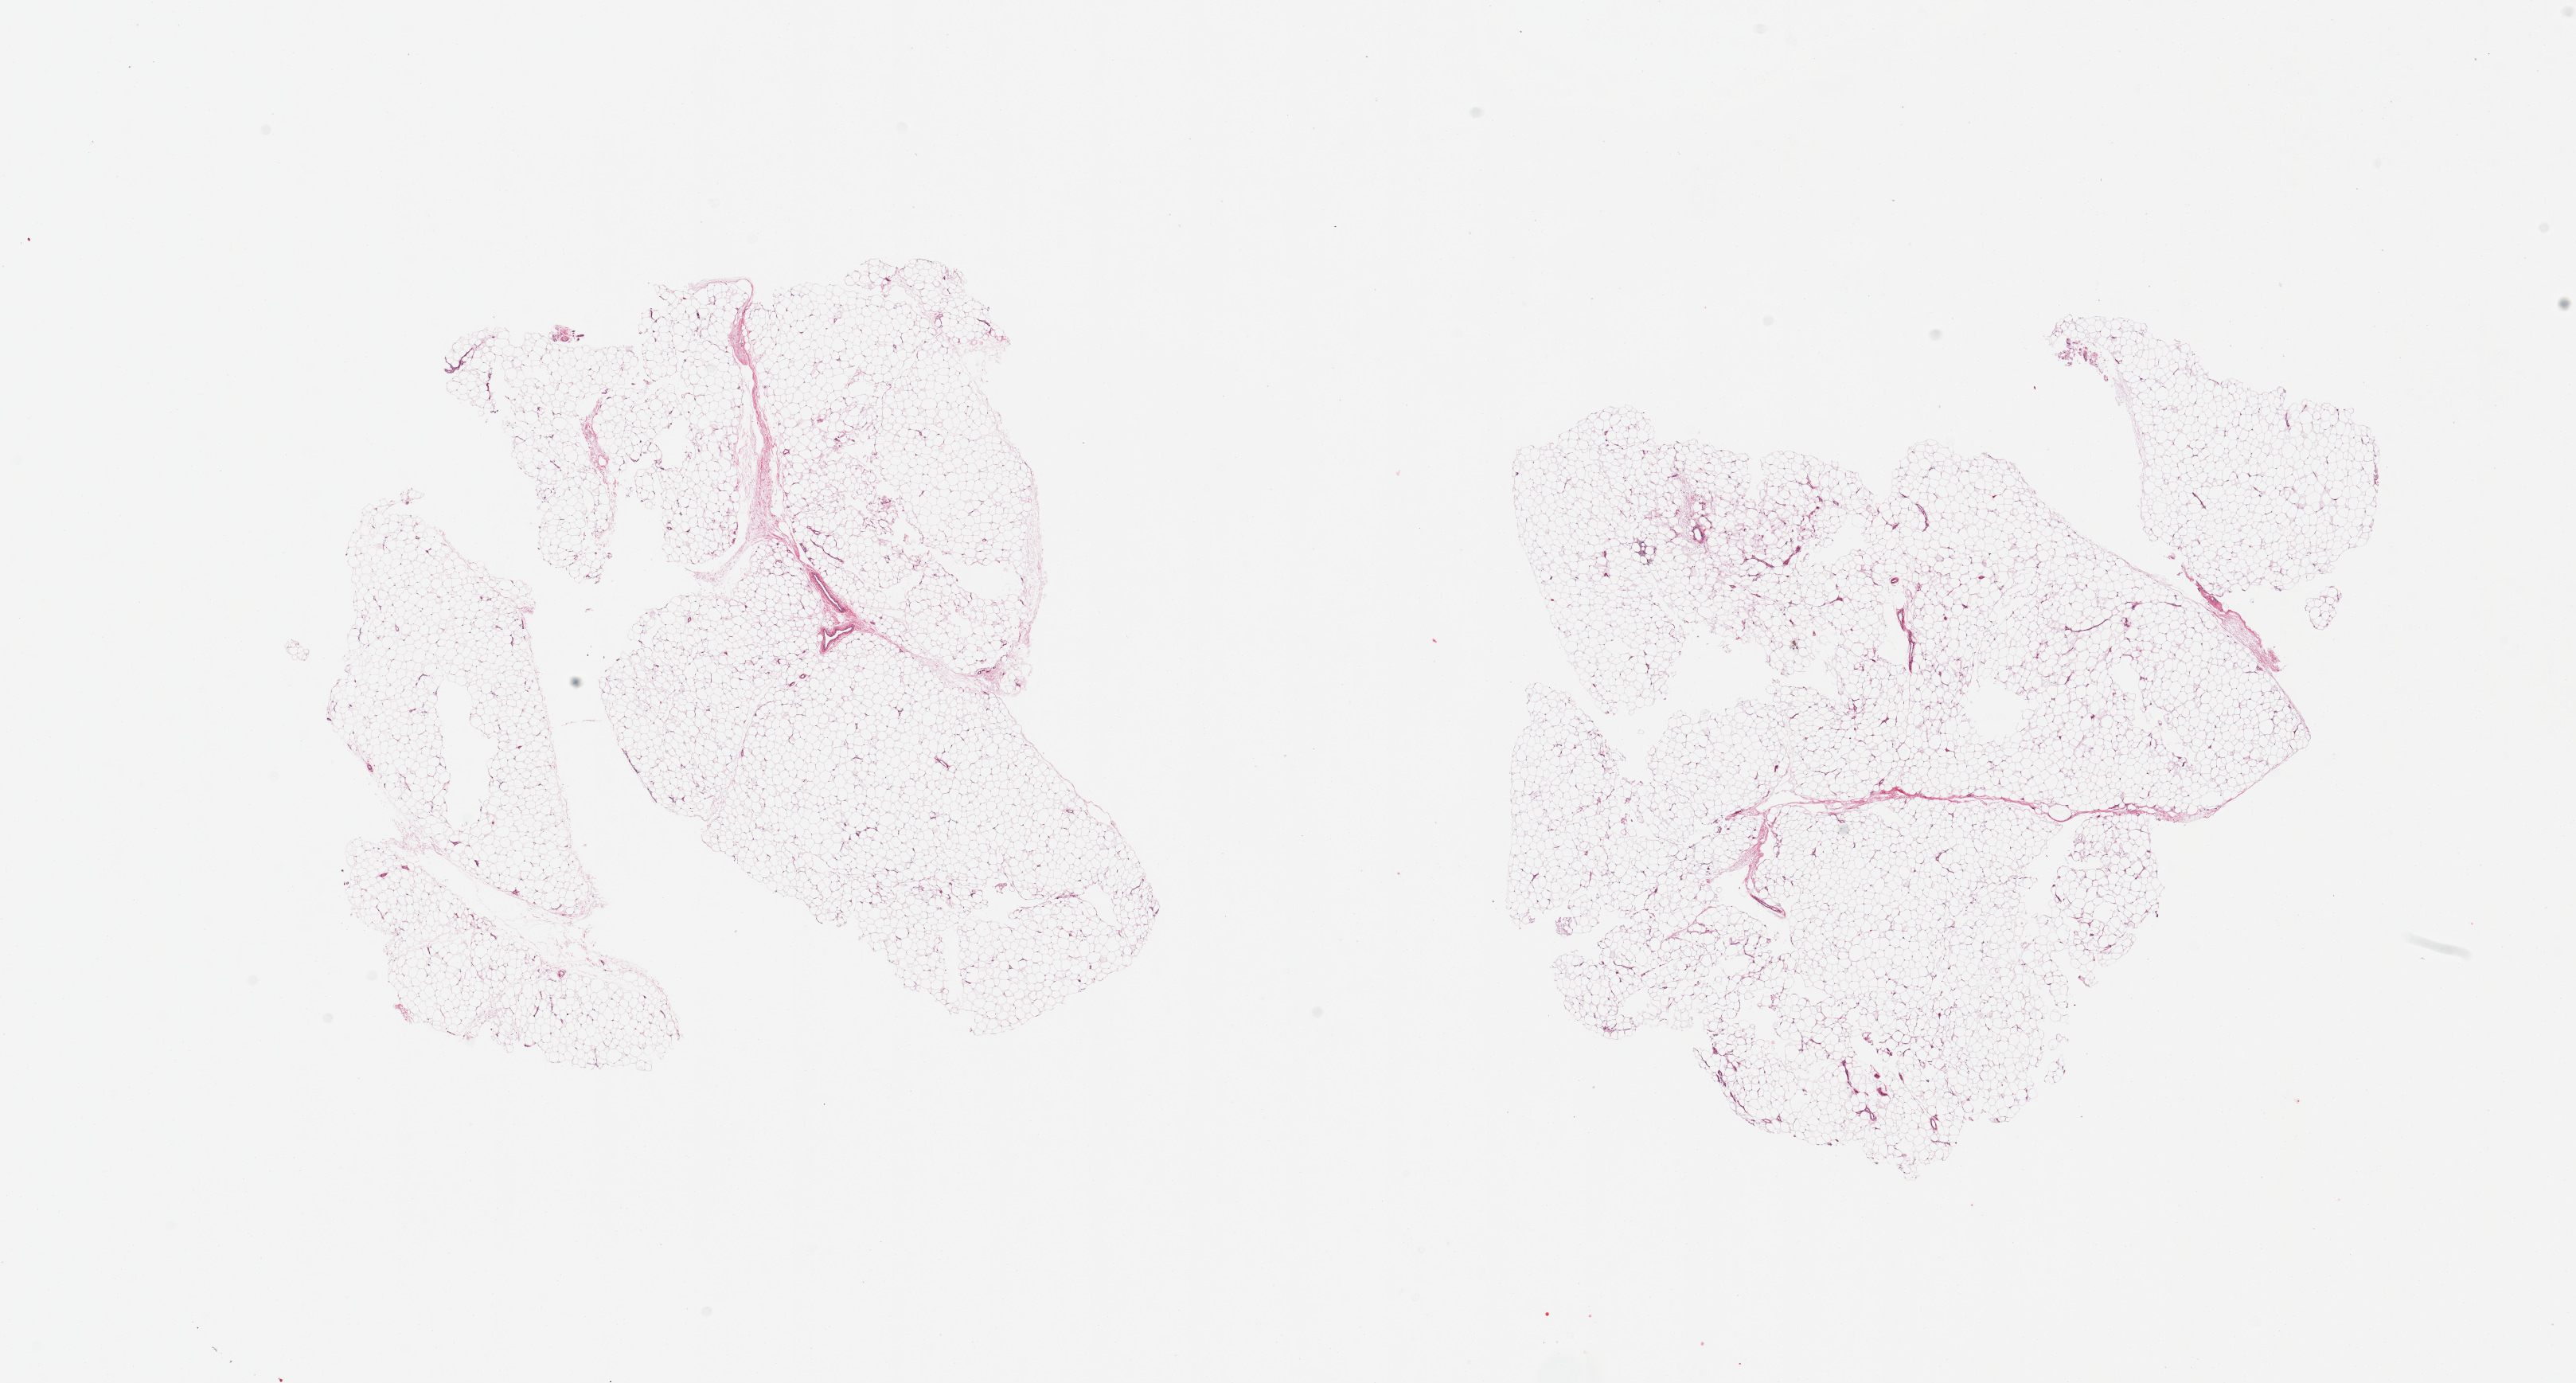
Digitized hematoxylin and eosin (H&E)-stained section, a low-resolution overview of the entire scanned area, about 25.6 x 13.7 mm (acquisition: 20x scan); PAXgene-fixed, paraffin-embedded tissue; target tissue: adipose tissue; donor tissue sample. Donor sex: female.
Pathologist's review note for this sample: 2 pieces, minimal fascia.